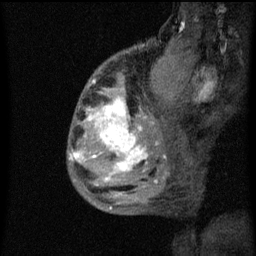
Breast MRI (dynamic contrast-enhanced), one sagittal slice; slice 18 of 60 in the series (ordered by position); dynamic contrast-enhanced series, image 2 of 3 at this slice position (ordered by acquisition); 1.5 T; TE 4.2 ms, TR 8 ms; 2 mm slice thickness; 256 × 256 image matrix, field of view 180 × 180 mm. Patient: female, 50 years.
Annotated regions visible in this slice (semi-automatic segmentation, software-assisted and operator-edited):
- analysis volume of interest (the breast-tissue region the enhancement analysis was run in; not a lesion): bounding box [x1, y1, x2, y2] px = [68, 64, 141, 187]
- tumour enhancement mask (voxels above the 70 % enhancement threshold inside the analysis volume of interest): [69, 96, 141, 181]